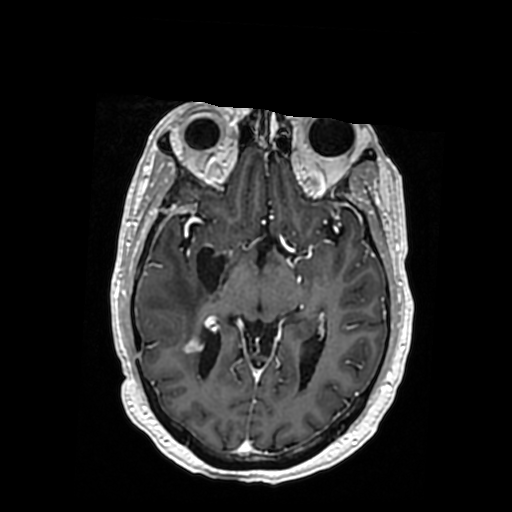
Brain MRI from a brain-tumour surgery series, one axial slice; position 200 of 364 along the scan axis; T1-weighted post-contrast; 512 × 512 image matrix, field of view 260 × 260 mm. From the clinical record (not read from this slice): histopathology: Oligodendroglioma; WHO grade: 3; IDH mutation: yes; tumour location: Right Posterior Temporal Inferior Parietal.
Outlined on this slice (expert manual segmentation):
- previous resection cavity: bounding box [x1, y1, x2, y2] px = [196, 246, 228, 292]
- tumour: [196, 336, 214, 348]